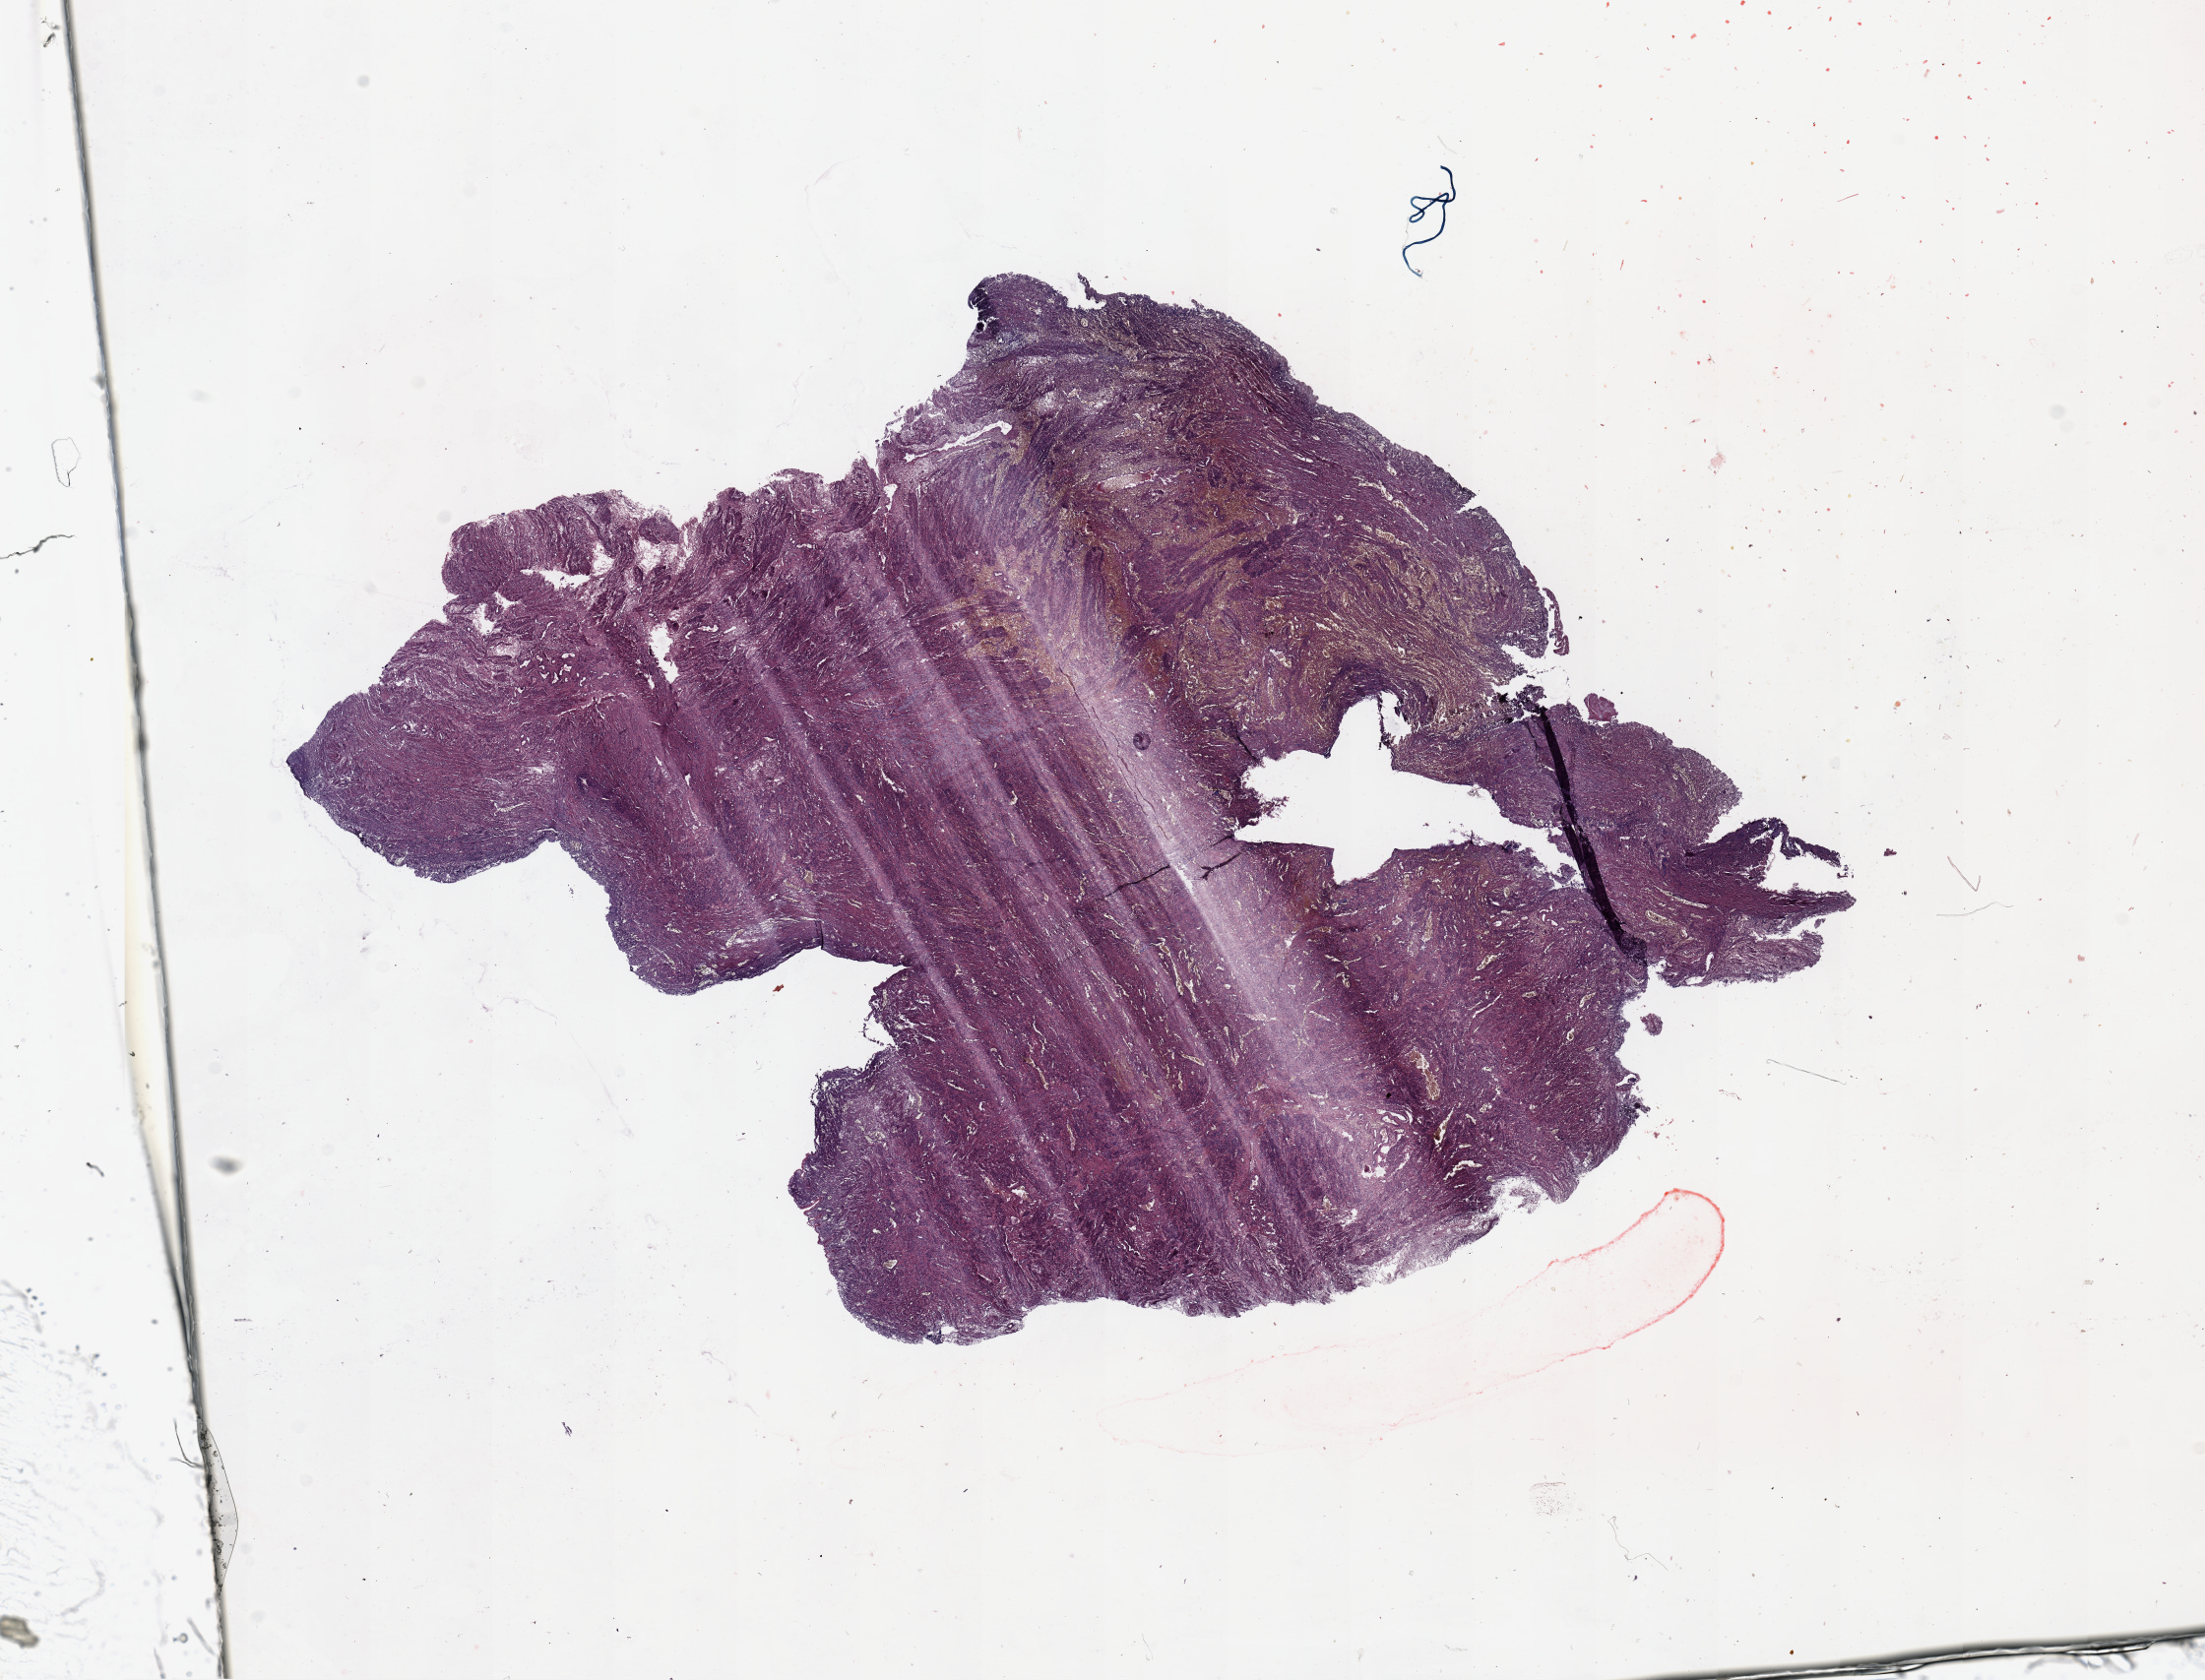
H&E-stained whole-slide image, whole scanned area (about 17.7 x 13.5 mm, slide scanned at 20x) shown as a low-resolution overview, normal (non-tumour) tissue sample, sampled site: uterus. 70-year-old female patient.
This section: normal (non-tumour) tissue from the same patient. Patient diagnosis: Endometrioid adenocarcinoma, NOS.